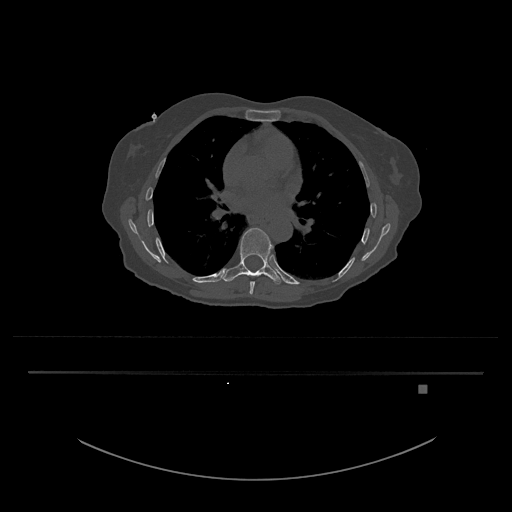
CT including the spine, one axial slice. Position 771 of 797 along the scan axis. 120 kVp. Bone window (W 1800 / L 400 HU). 0.5 mm slice thickness. 512 × 512 image matrix, field of view 500 × 500 mm. Patient: female, 57 years. Case-level facts recorded for this patient, not image findings: primary cancer: cervical.
Outlined on this slice (semi-automatic segmentation, software-assisted and operator-edited):
- T8 vertebra: bounding box [x1, y1, x2, y2] px = [249, 281, 255, 295]
- T9 vertebra: [223, 228, 283, 285]